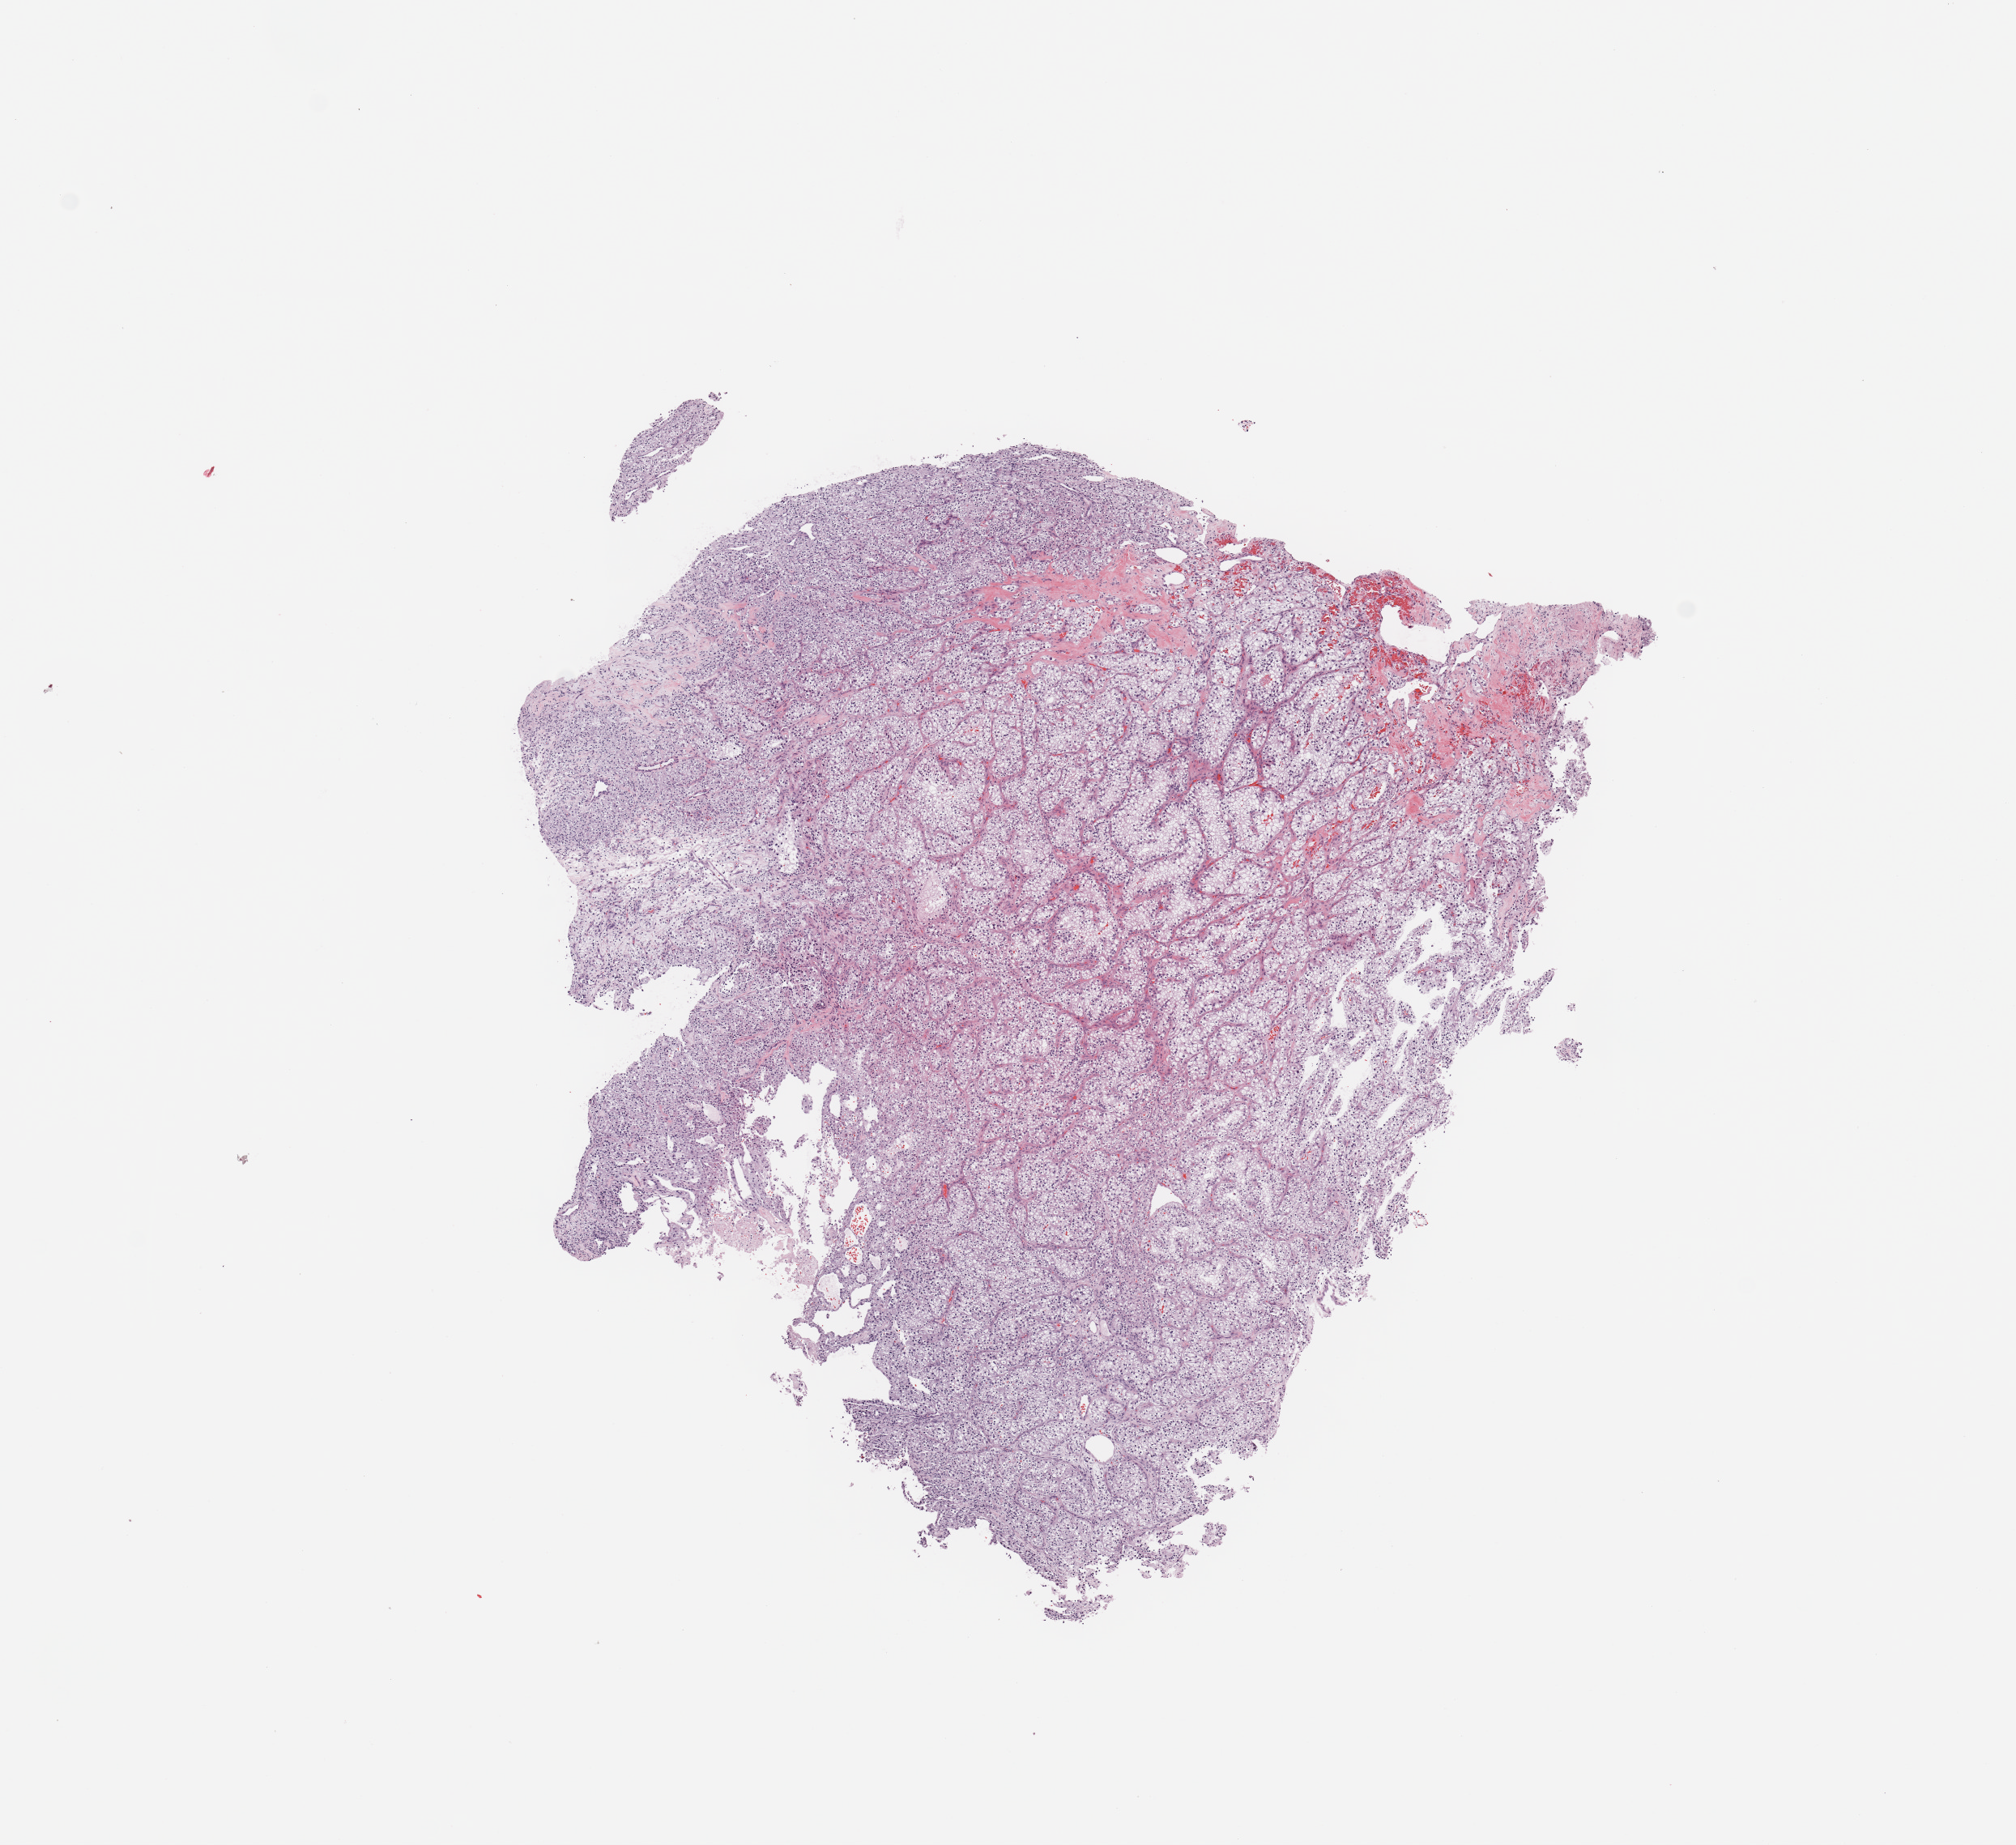
Hematoxylin and eosin (H&E) stained whole-slide image, a low-resolution overview of the entire scanned area, about 9.8 x 9.0 mm (acquisition: 20x scan); tumour tissue sample, sampled site: kidney. 61-year-old male patient.
Histologic diagnosis: Renal cell carcinoma, NOS.